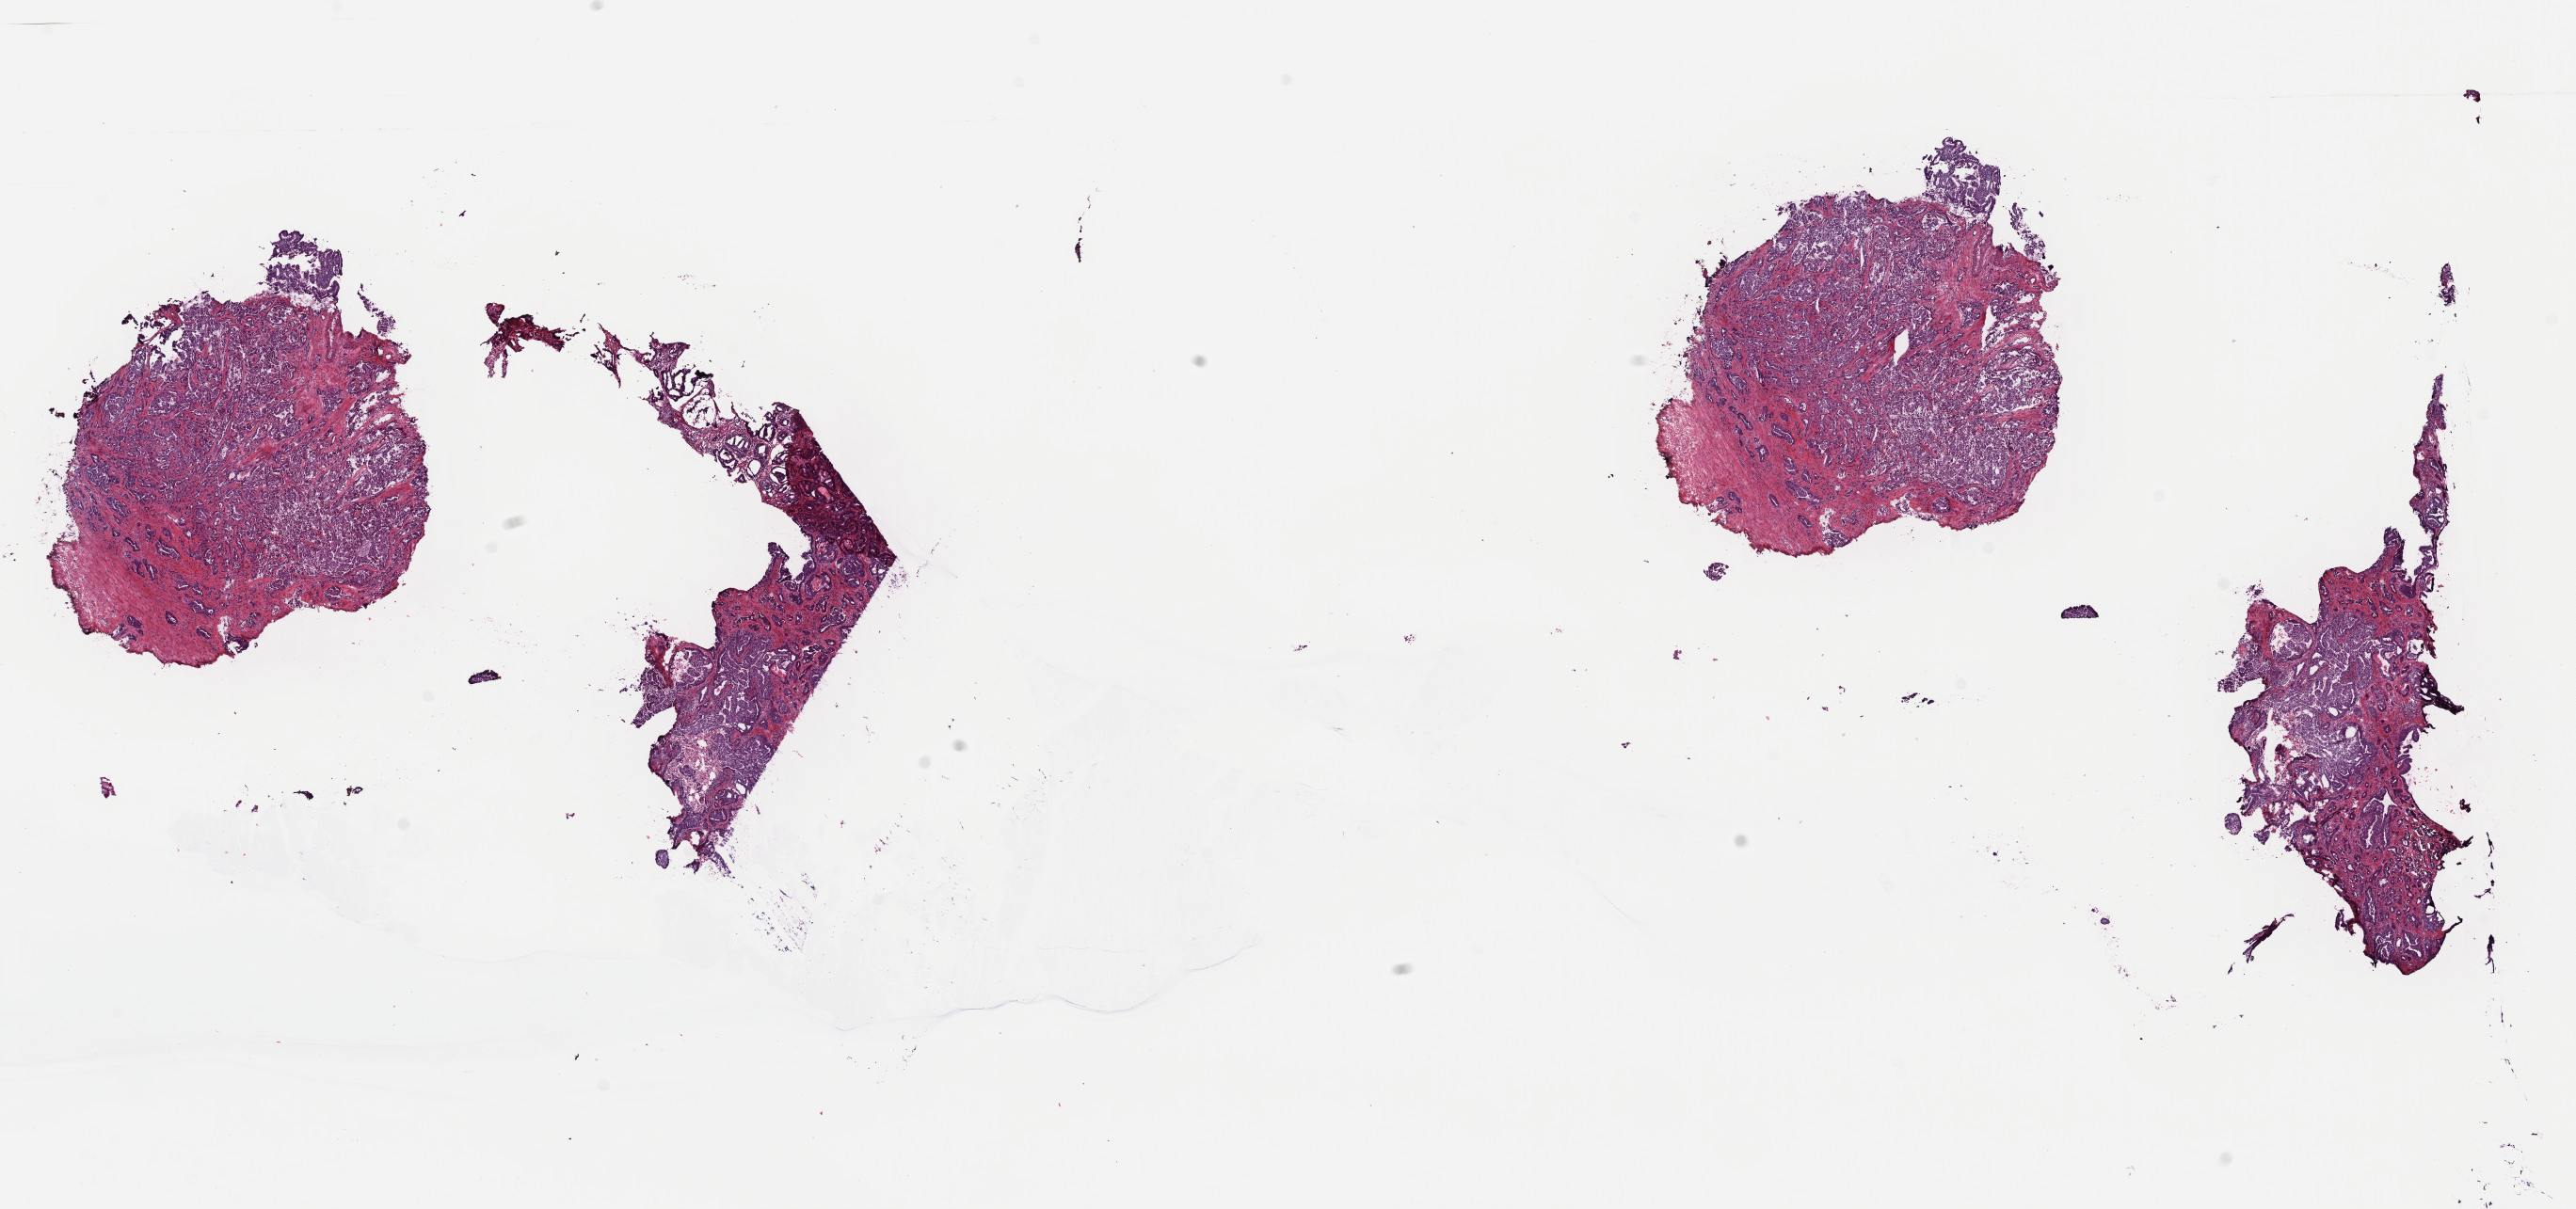
Digitized H&E tissue section (whole slide) — low-resolution overview of the scanned area, about 21.6 x 10.1 mm, frozen section from the top of the tissue portion, sample: primary tumour, prostate. Male patient; age at initial diagnosis 56 years. Gleason score: 7 (4+3). Pathologist review of this section (percent, as recorded): tumour cells 80%, tumour nuclei 80%, normal cells 0%, stromal cells 20%, necrosis 0%. Inflammatory infiltration, as recorded: lymphocyte infiltration 40%, monocyte infiltration 20%, neutrophil infiltration 20%.
• laterality: bilateral
• lymph nodes positive (case pathology): 0 of 11 examined
• pathologic diagnosis: Adenocarcinoma, NOS (prostate gland)